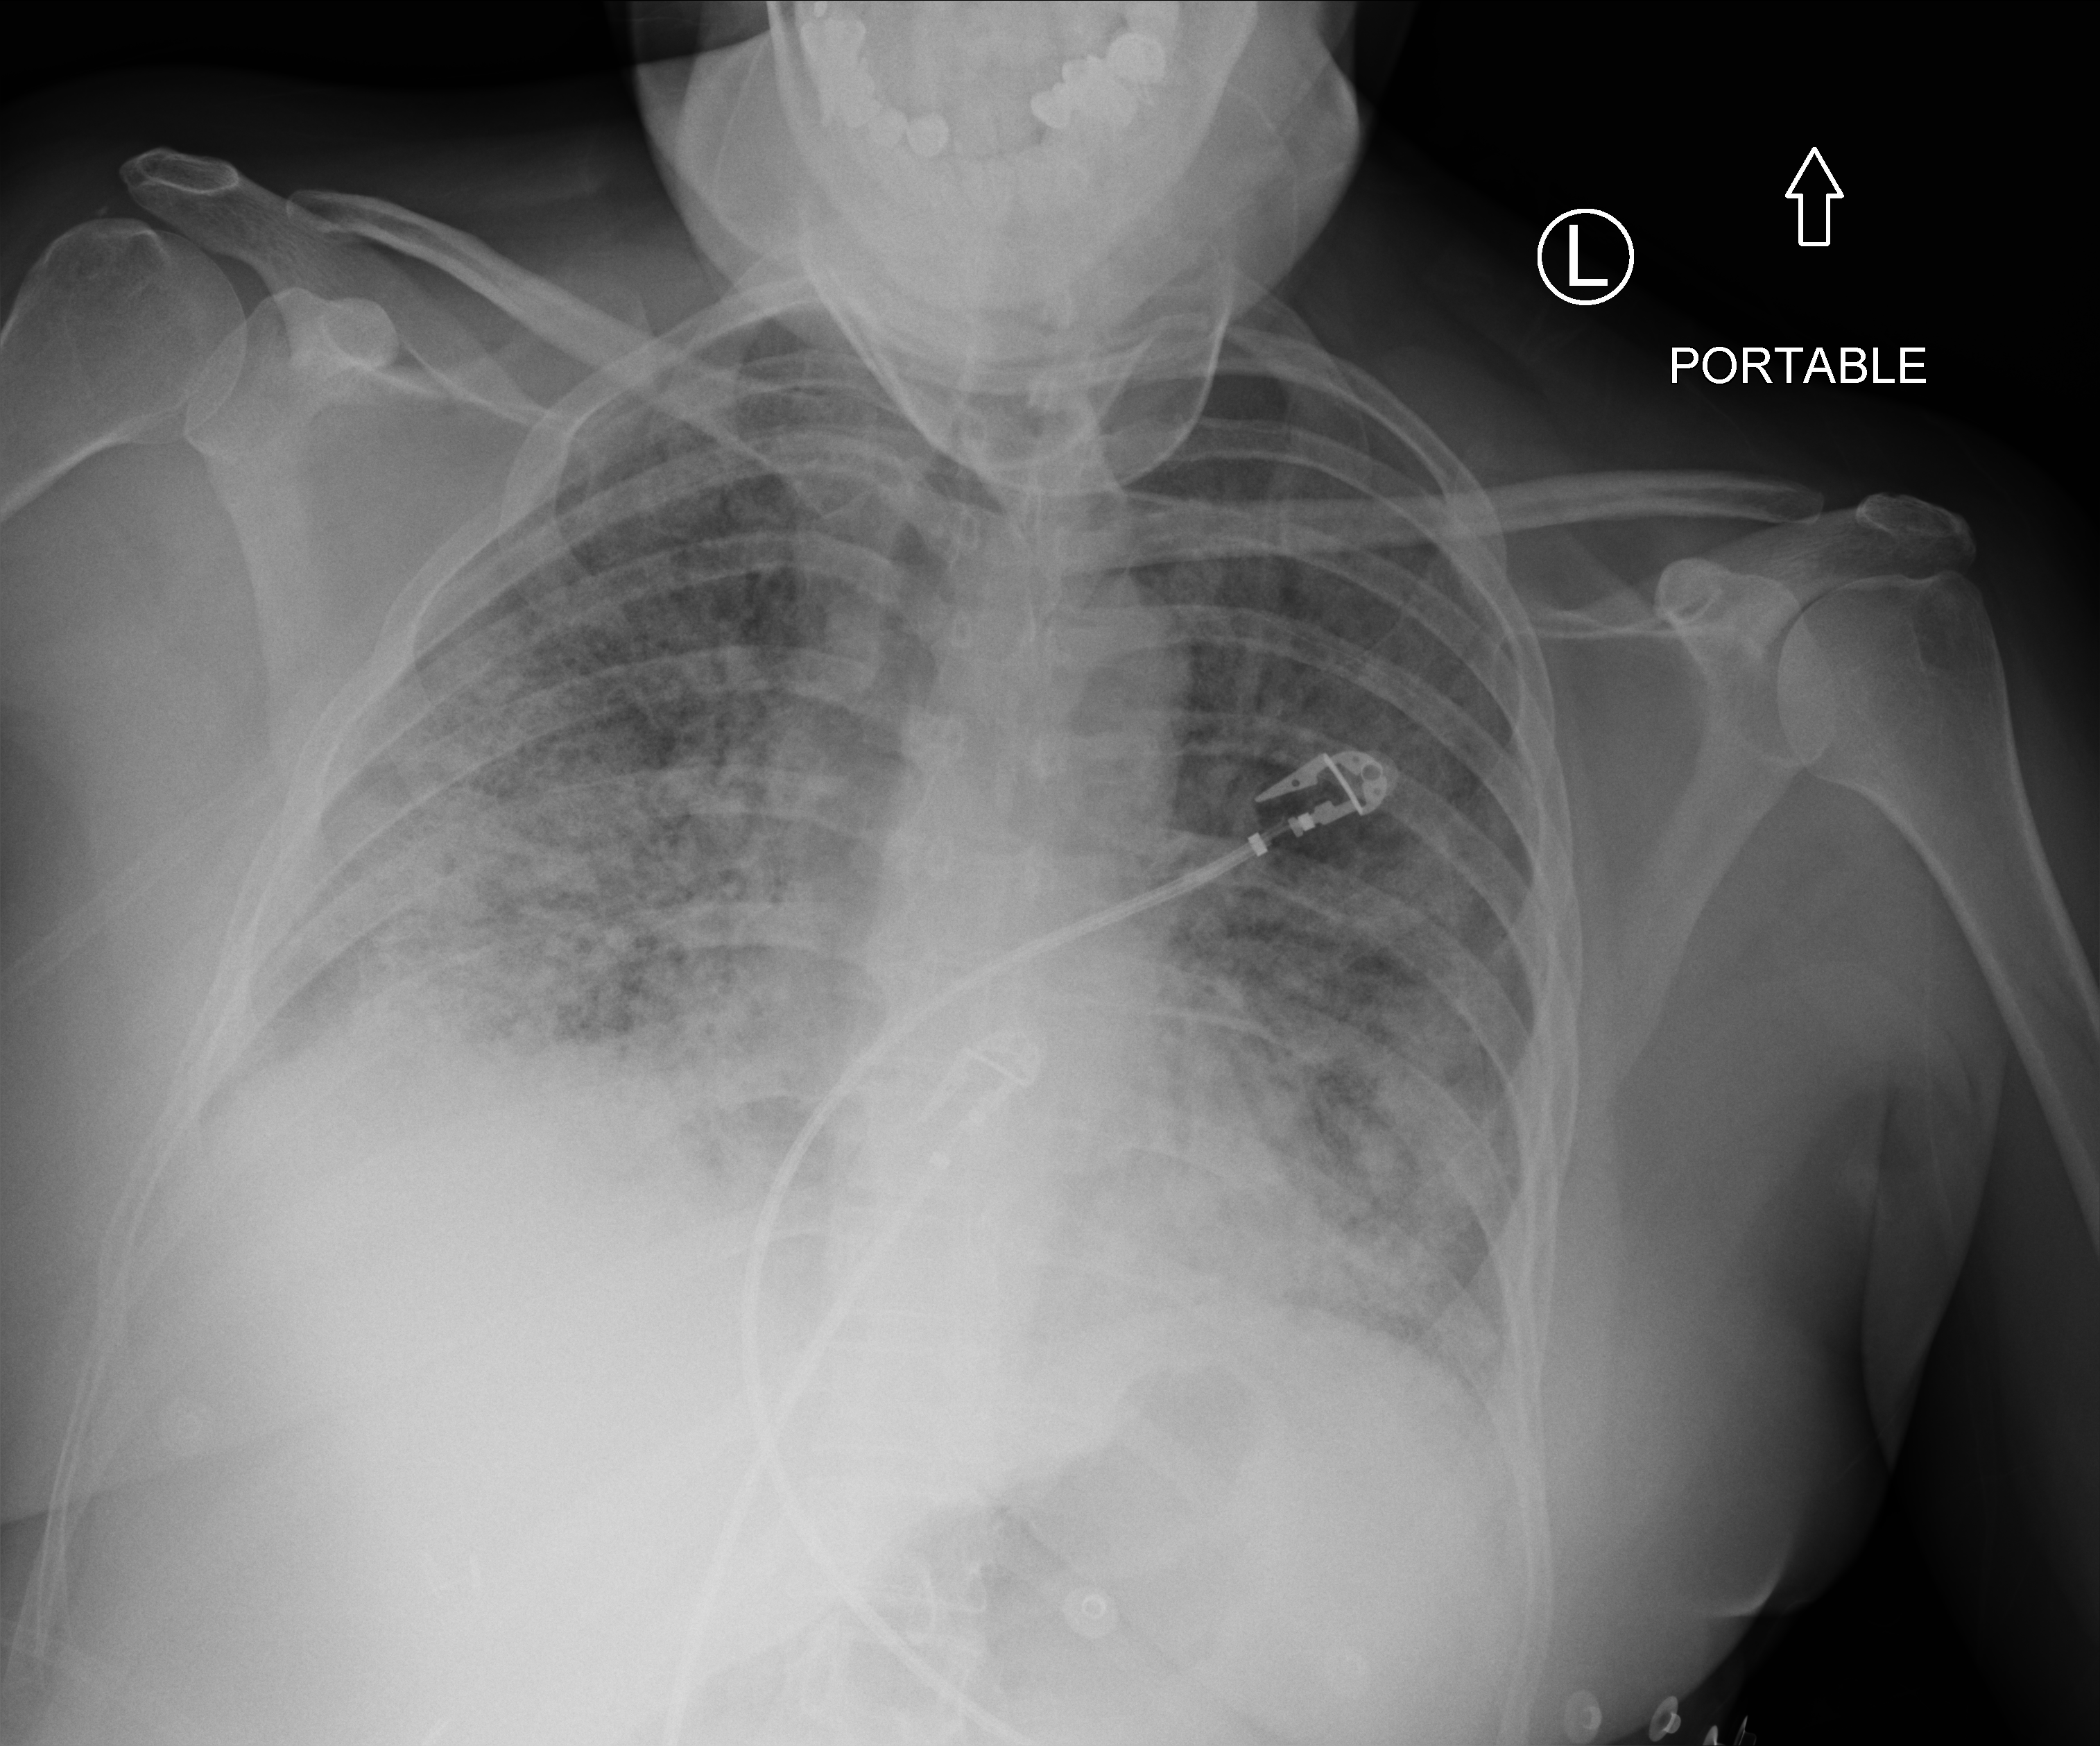
Chest X-ray (portable); anteroposterior (AP) projection. Patient hospitalised with COVID-19; female, aged 18–59 years.
From the hospital-stay record, not from the radiograph (when in the stay this image was taken is not recorded): mechanically ventilated during this hospital stay: no.